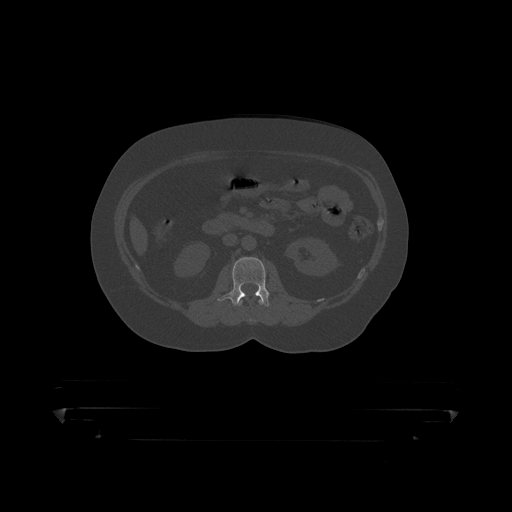
CT including the spine, one axial slice; slice 123 of 390 in the series (ordered by position); reconstruction kernel STANDARD; 120 kVp; bone window (W 1800 / L 400 HU); 512 × 512 image matrix, field of view 650 × 650 mm. Male patient, age 60 years. From the clinical record (not read from this slice): primary cancer: prostate.
Outlined on this slice (semi-automatically segmented with operator editing):
- L1 vertebra: bounding box (x1, y1, x2, y2) in pixels: (239, 299, 264, 307)
- L2 vertebra: (218, 258, 270, 308)